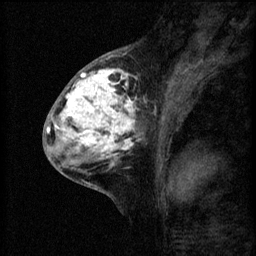
Breast MRI (dynamic contrast-enhanced), one sagittal slice; slice 28 of 60 in the series (ordered by position); 3 images stored at this slice position (order not interpretable as contrast timing); 1.5 T; TE 4.2 ms, TR 8.2 ms; 2 mm slice thickness; 256 × 256 image matrix. Female patient, age 41 years.
Outlined on this slice (semi-automatic segmentation, software-assisted and operator-edited):
- analysis volume of interest (the breast-tissue region the enhancement analysis was run in; not a lesion): bounding box (x1, y1, x2, y2) in pixels: (53, 62, 159, 175)
- tumour enhancement mask (voxels above the 70 % enhancement threshold inside the analysis volume of interest): (53, 68, 139, 167)